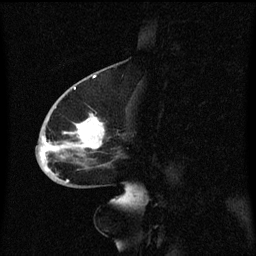
Breast MRI (dynamic contrast-enhanced), one sagittal slice; slice 29 of 60 in the series (ordered by position); dynamic contrast-enhanced series, image 2 of 3 at this slice position (ordered by acquisition); 1.5 T; TE 4.2 ms, TR 8.4 ms; 2 mm slice thickness; 256 × 256 image matrix, field of view 200 × 200 mm. Patient: female, 68 years. Case-level facts recorded for this patient, not image findings: setting: breast cancer imaged before/during neoadjuvant chemotherapy; receptor status: triple-negative.
Structures marked on this image (semi-automatically segmented with operator editing):
- analysis volume of interest (the breast-tissue region the enhancement analysis was run in; not a lesion): bounding box <37,94,119,173> (left, top, right, bottom; pixels)
- tumour enhancement mask (voxels above the 70 % enhancement threshold inside the analysis volume of interest): <41,116,106,171>